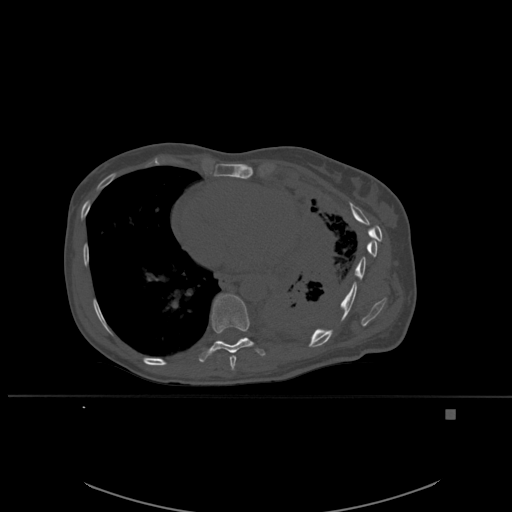
CT including the spine, one axial slice; position 334 of 537 along the scan axis; bone window (W 1800 / L 400 HU); 512 × 512 image matrix, field of view 440 × 440 mm. Patient: female, 45 years. From the clinical record (not read from this slice): primary cancer: lung.
Annotated regions visible in this slice (semi-automatically segmented with operator editing):
- T8 vertebra: bounding box [x1, y1, x2, y2] px = [229, 355, 237, 370]
- T9 vertebra: [198, 293, 265, 362]